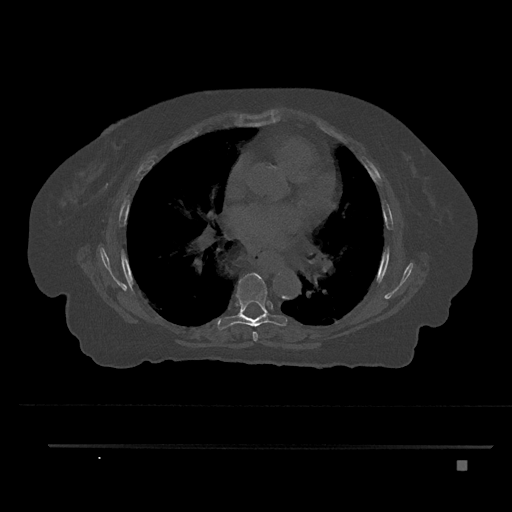
CT including the spine, one axial slice. Slice 492 of 797 in the series (ordered by position). 120 kVp. Bone window (W 1800 / L 400 HU). 0.5 mm slice thickness. 512 × 512 image matrix. Patient: female, 76 years. From the clinical record (not read from this slice): primary cancer: lung.
Outlined on this slice (semi-automatically segmented with operator editing):
- T6 vertebra: box from (x=252, y=331) to (x=258, y=341) px
- T7 vertebra: (x=217, y=273)–(x=288, y=331)
- T8 vertebra: (x=245, y=315)–(x=261, y=317)